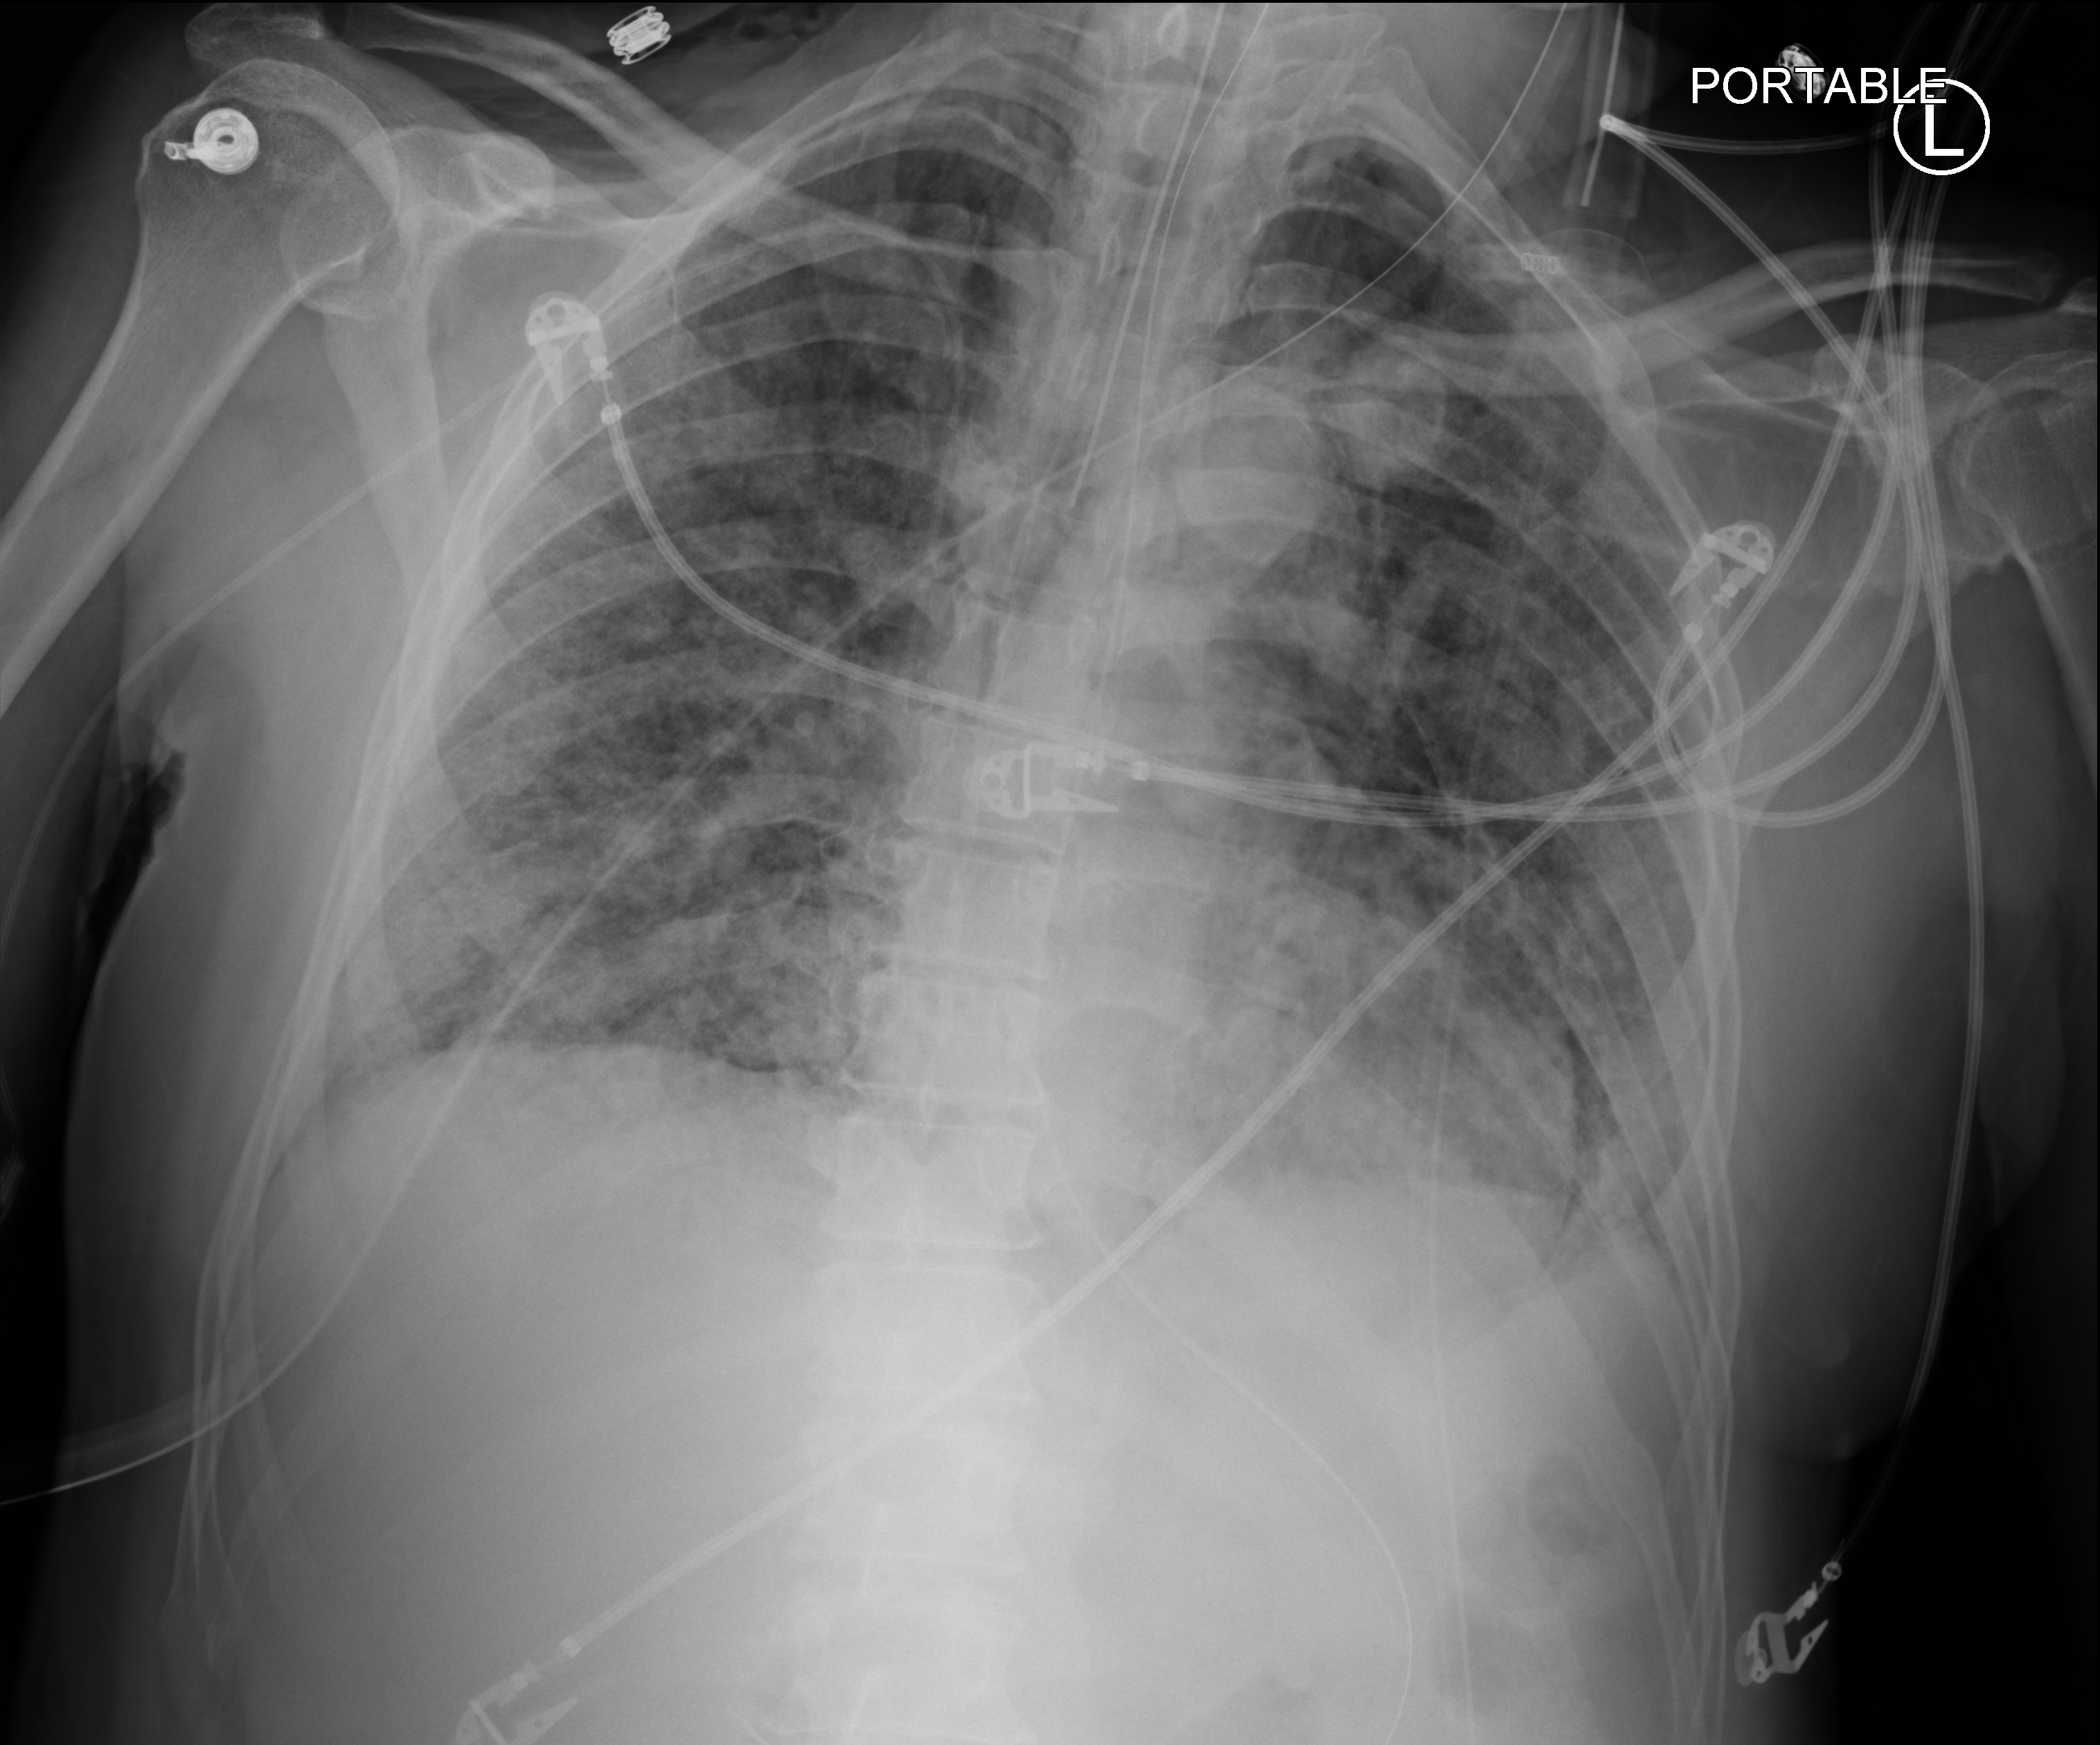
Chest X-ray (portable), anteroposterior (AP) projection. Patient hospitalised with COVID-19; male, aged 60–74 years.
Admission-level facts for this patient (not findings on this image; timing relative to this image not recorded): admitted to intensive care during this hospital stay: yes.